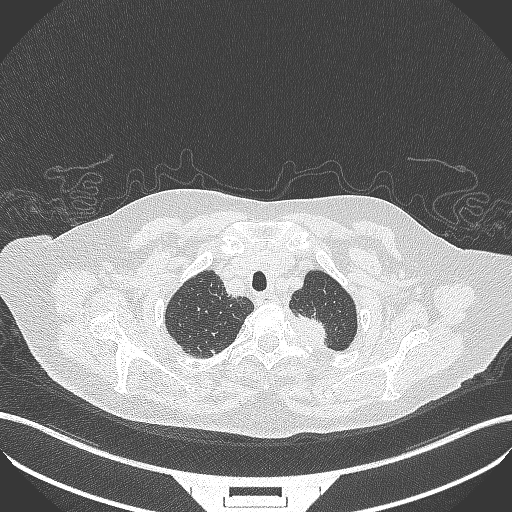
Chest CT, one axial slice; slice 305 of 353 in the series (ordered by position); reconstruction kernel B70f; lung window (W 1500 / L -600 HU); 512 × 512 image matrix, field of view 400 × 400 mm. Female patient, age 81 years. Case-level facts recorded for this patient, not image findings: clinical TNM (as recorded): T2a N0 M0.
Annotated regions visible in this slice (bounding box drawn by a radiologist):
- lung tumour (recorded histology: adenocarcinoma): bounding box (x1, y1, x2, y2) in pixels: (287, 312, 335, 348)